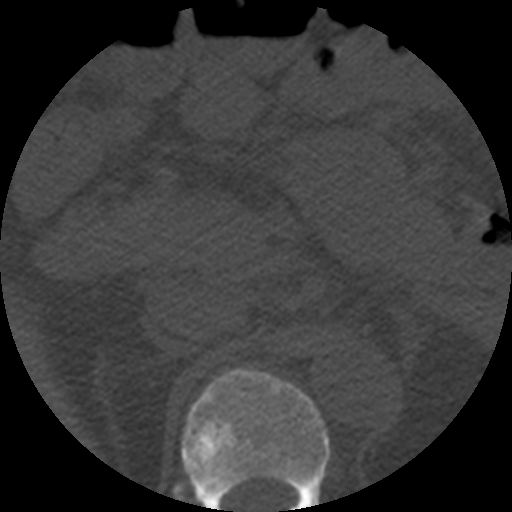
CT including the spine, one axial slice. Slice 222 of 508 in the series (ordered by position). 120 kVp. Bone window (W 1800 / L 400 HU). 1.25 mm slice thickness. 512 × 512 image matrix. Patient age 57 years. Case-level facts recorded for this patient, not image findings: primary cancer: prostate.
Structures marked on this image (semi-automatic segmentation, software-assisted and operator-edited):
- T12 vertebra: bounding box <181,368,331,512> (left, top, right, bottom; pixels)